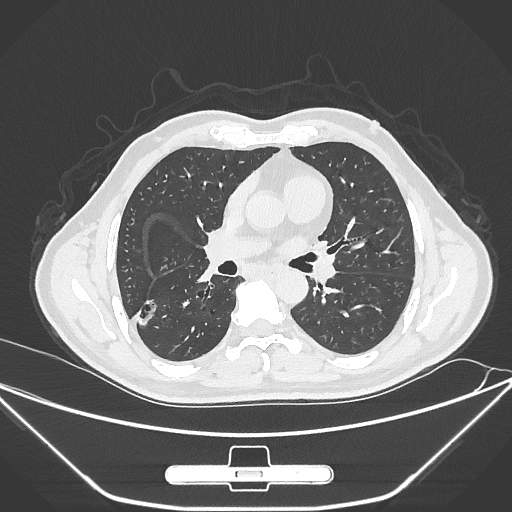
Chest CT, one axial slice; 120 kVp; lung window (W 1500 / L -600 HU); 512 × 512 image matrix. Male patient, age 71 years. Case-level facts recorded for this patient, not image findings: clinical TNM (as recorded): T1c N0 M0; histopathological grade: G2.
Outlined on this slice (bounding box drawn by a radiologist):
- lung tumour (recorded histology: adenocarcinoma): bounding box <130,295,159,338> (left, top, right, bottom; pixels)